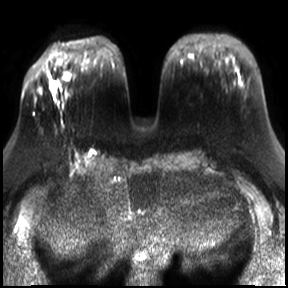
Breast MRI, one axial slice. Diffusion-weighted series; image 2 of 4 stored at this slice position (different b-values; order by instance number). 3 T. 4 mm slice thickness. 288 × 288 image matrix, field of view 340 × 340 mm. Female patient.
Outlined on this slice (expert manual segmentation):
- tumour on diffusion-weighted imaging: box from (x=51, y=80) to (x=55, y=87) px